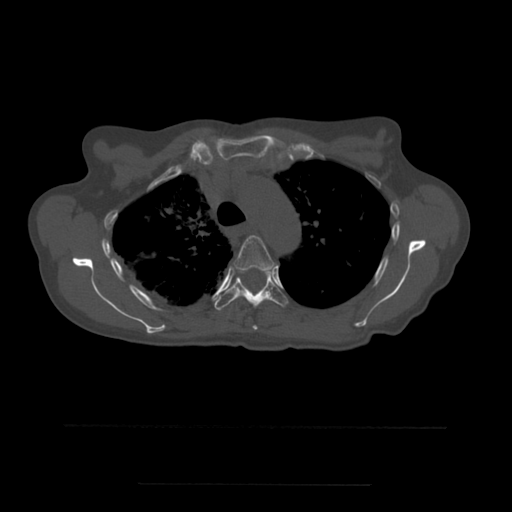
CT including the spine, one axial slice. Bone window (W 1800 / L 400 HU). 1.25 mm slice thickness. 512 × 512 image matrix. Patient age 58 years. Case-level facts recorded for this patient, not image findings: primary cancer: lung.
Annotated regions visible in this slice (semi-automatic segmentation, software-assisted and operator-edited):
- T4 vertebra: box from (x=234, y=236) to (x=275, y=330) px
- T5 vertebra: (x=215, y=270)–(x=288, y=311)